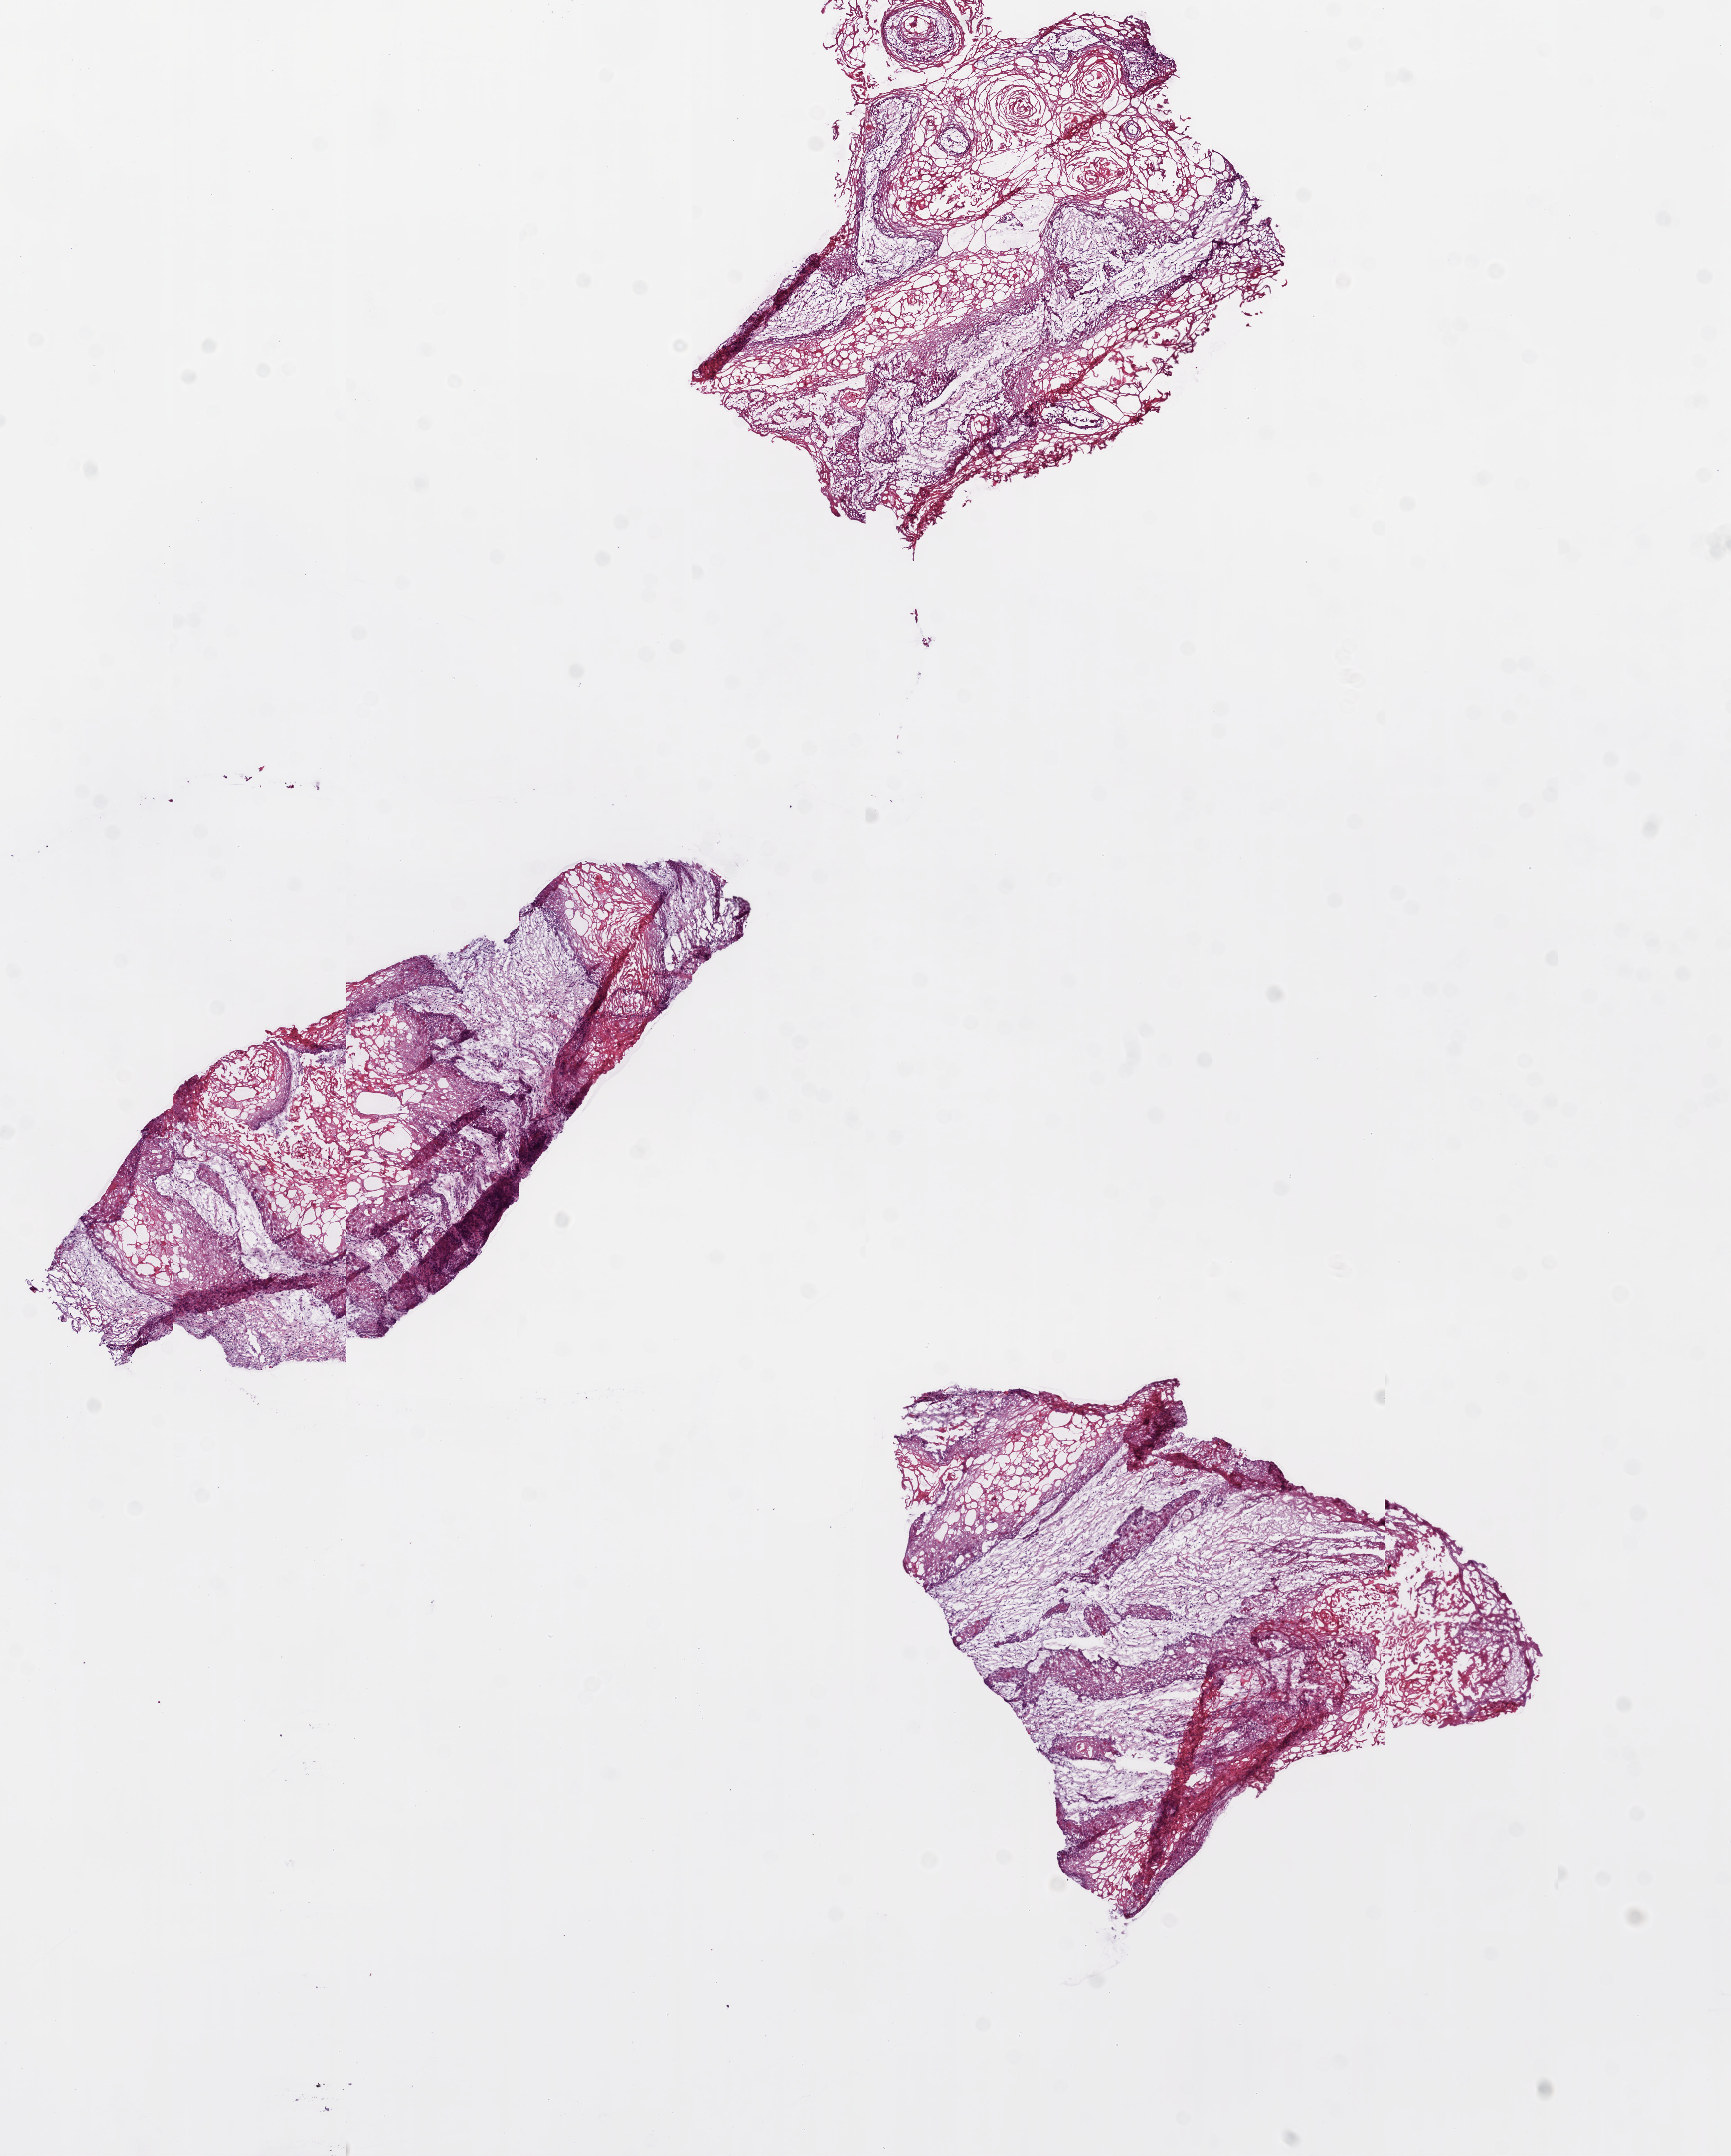
Digitized H&E tissue section (whole slide), low-resolution overview of the scanned area, about 10.0 x 12.5 mm (slide scanned at 20x). Frozen section from the bottom of the tissue portion. Primary tumour sample from the head and neck. Male patient; age at initial diagnosis 68 years. Histologic grade: G2 (moderately differentiated). Composition of this section per pathologist review: tumour cells 70%, tumour nuclei 85%, normal cells 0%, stromal cells 30%, necrosis 0%.
- lymph nodes positive (case pathology): 6 of 14 examined
- AJCC pathologic stage: IVA (7th edition)
- pathologic diagnosis: Squamous cell carcinoma, NOS